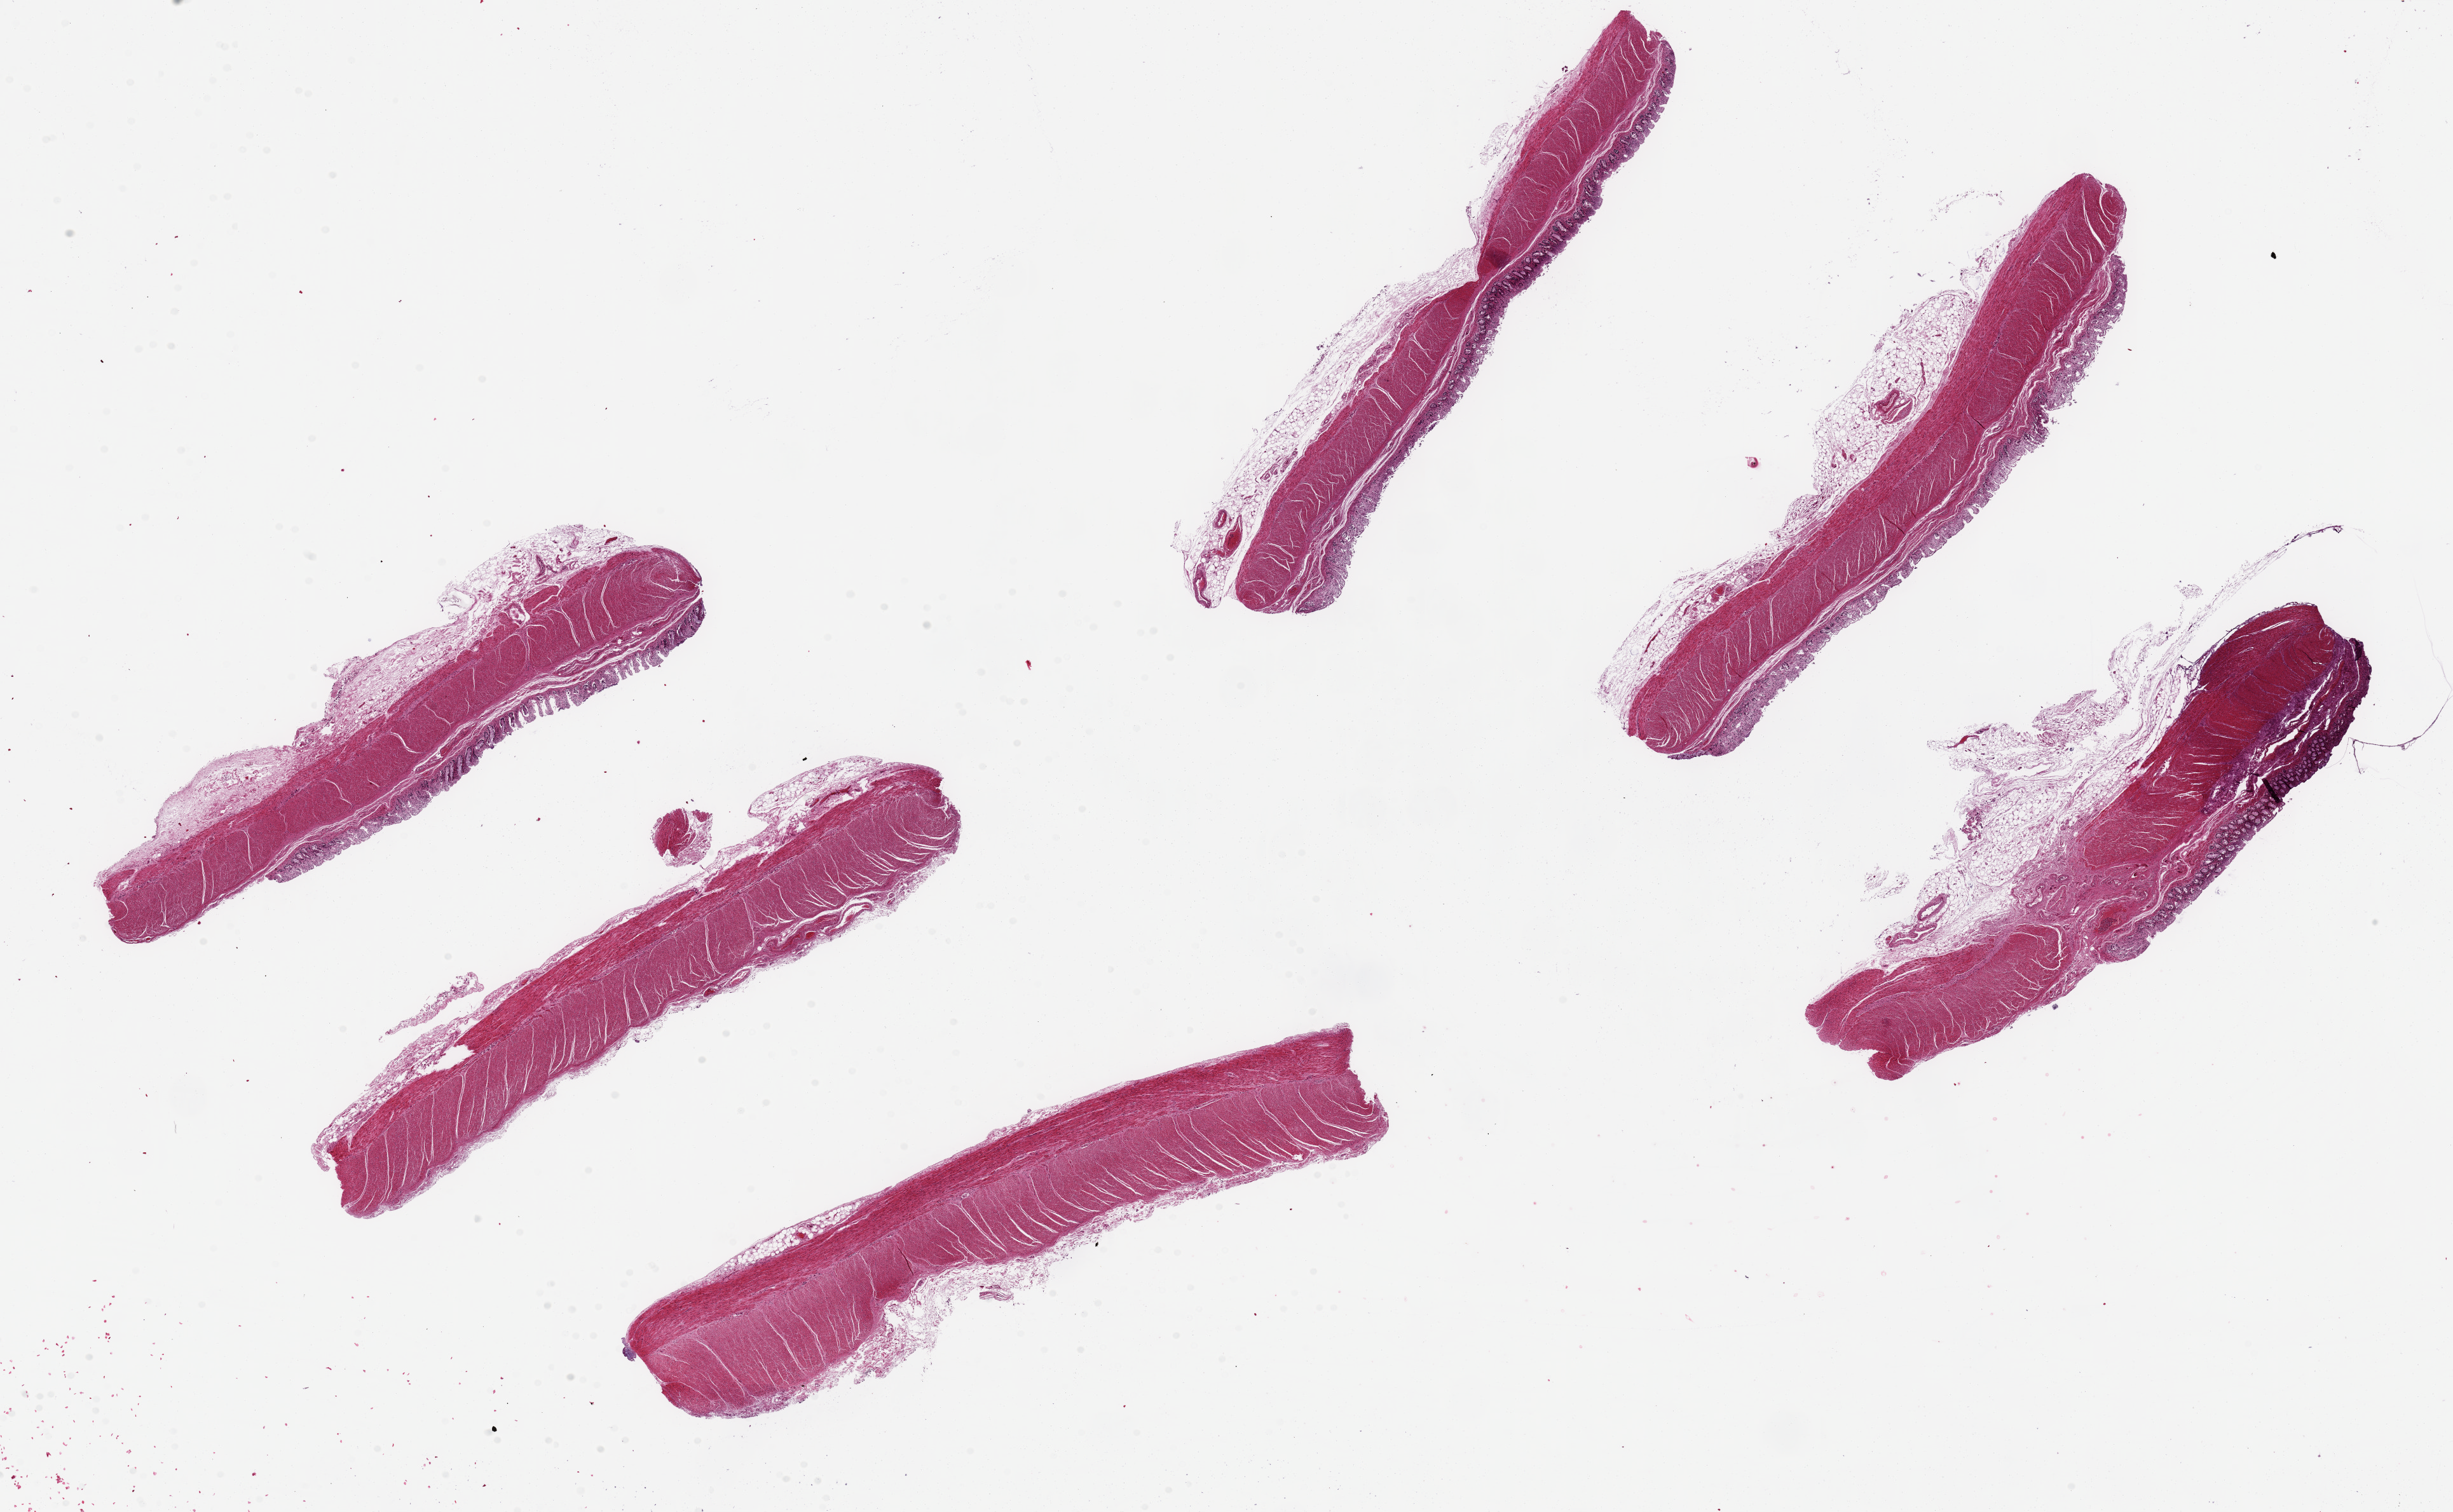
Digitized hematoxylin and eosin (H&E)-stained section, whole scanned area (about 30.5 x 18.8 mm) shown as a low-resolution overview; PAXgene-fixed paraffin-embedded (PFPE) section; sampled site (target tissue): transverse colon; donor tissue sample. Donor sex: female.
* review note (as recorded): 6 ~9x2mm pieces. Mucosa sloughed in >50%; where present, badly autolyzed, score three, ~10% of thickness. Areas of poor/under-fixation